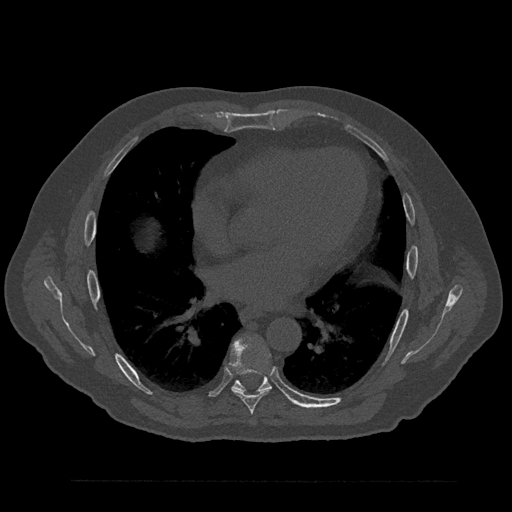
CT including the spine, one axial slice. Position 486 of 797 along the scan axis. Reconstruction kernel Br40s/3. 120 kVp. Bone window (W 1800 / L 400 HU). 0.5 mm slice thickness. 512 × 512 image matrix. Patient: male, 61 years. From the clinical record (not read from this slice): primary cancer: prostate.
Annotated regions visible in this slice (semi-automatically segmented with operator editing):
- T7 vertebra: bounding box [x1, y1, x2, y2] px = [230, 339, 272, 414]
- T8 vertebra: [232, 376, 272, 392]